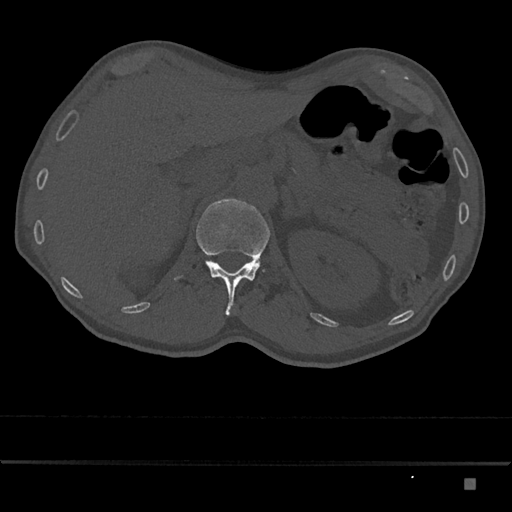
CT including the spine, one axial slice; position 543 of 797 along the scan axis; reconstruction kernel Br40s/3; 120 kVp; bone window (W 1800 / L 400 HU); 512 × 512 image matrix. Male patient, age 72 years. From the clinical record (not read from this slice): primary cancer: prostate.
Outlined on this slice (semi-automatically segmented with operator editing):
- L1 vertebra: bounding box (x1, y1, x2, y2) in pixels: (196, 198, 270, 316)